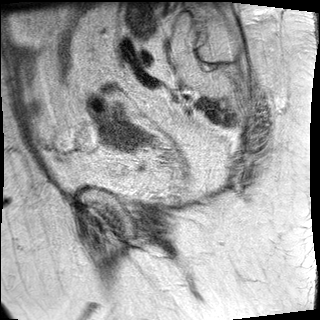
Pelvic MRI for cervical cancer, one sagittal slice. Slice 9 of 27 in the series (ordered by position). T2-weighted. 1.5 T. TE 89 ms, TR 2740 ms. 4 mm slice thickness. 320 × 320 image matrix, field of view 260 × 260 mm. Patient: female, 67 years.
Outlined on this slice (manually delineated by an expert):
- uterus and cervix: box from (x=99, y=119) to (x=147, y=152) px